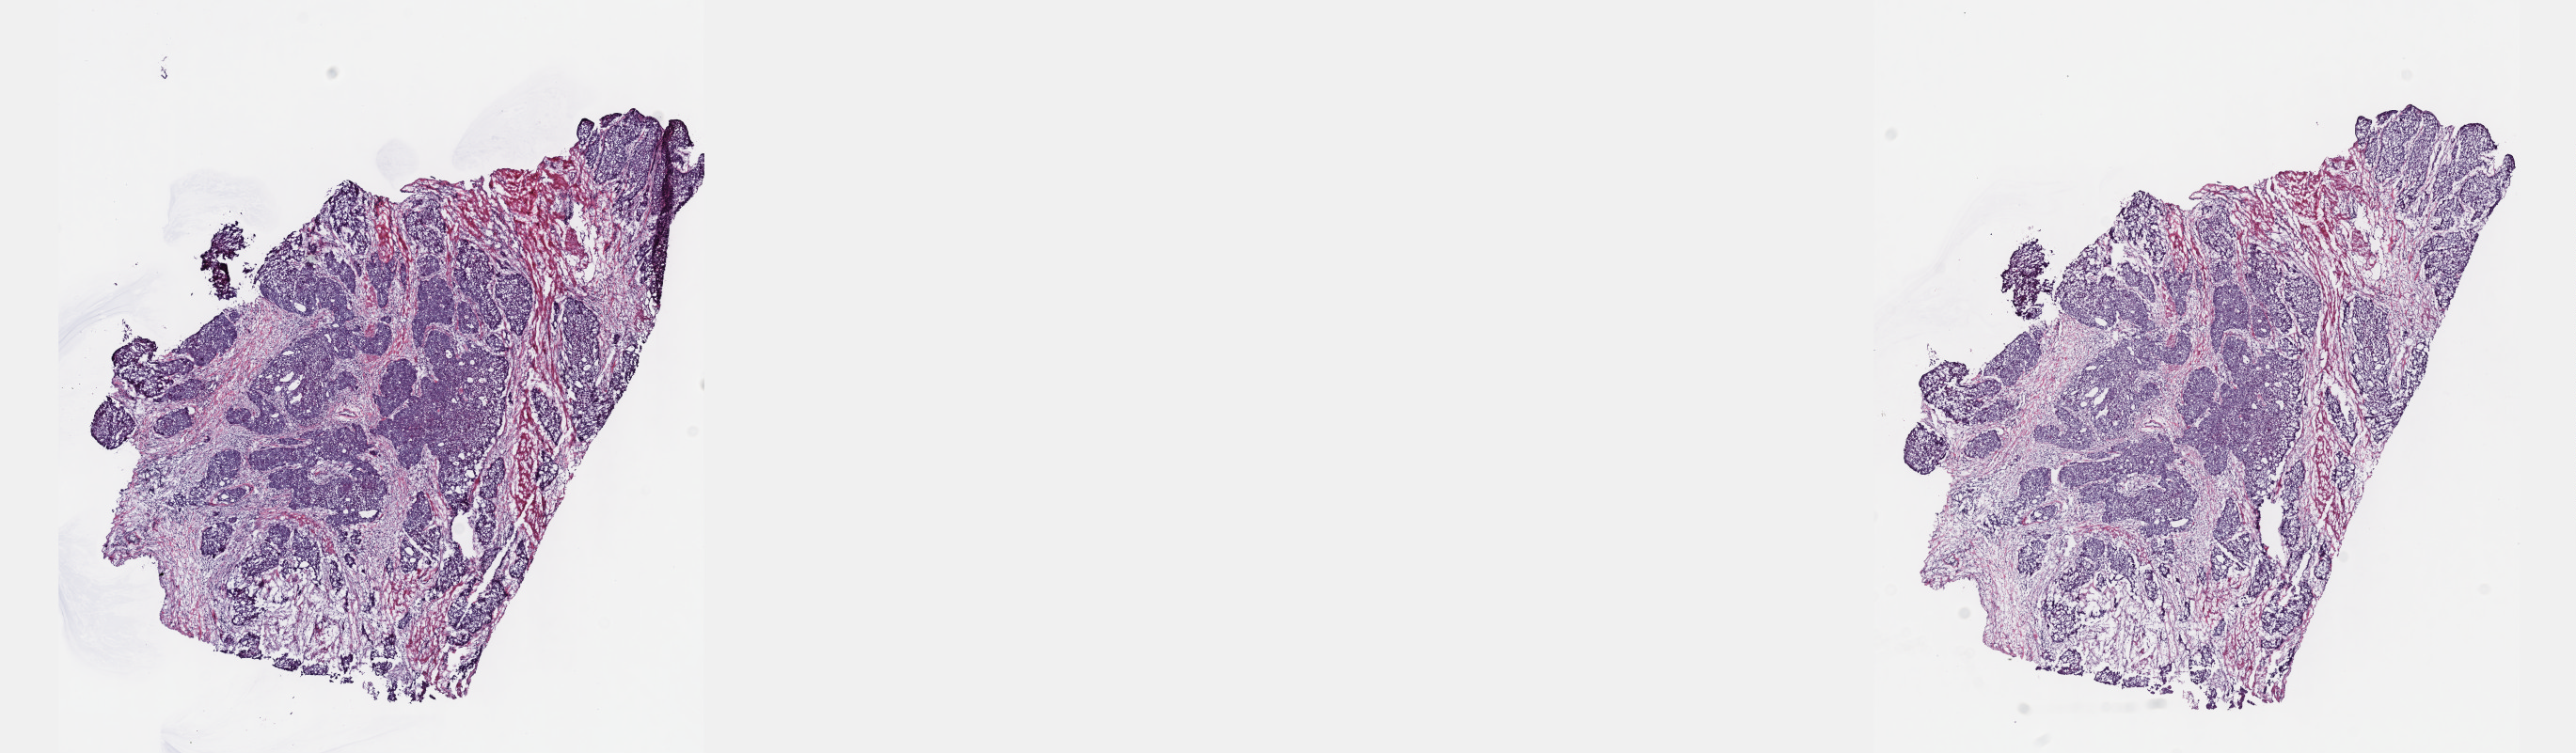
Whole-slide histology image, Hematoxylin and eosin (H&E) stained — whole scanned area (about 22.1 x 6.5 mm) shown as a low-resolution overview; frozen section from the top of the tissue portion; bladder, primary tumour sample. Patient: male, age at initial diagnosis 68 years. Histologic grade: high grade. Pathologist review of this section (percent, as recorded): tumour cells 75%, tumour nuclei 75%, normal cells 0%, stromal cells 25%, necrosis 0%. Inflammatory infiltration, as recorded: lymphocyte infiltration 2%, monocyte infiltration 1%, neutrophil infiltration 5%.
• pathologic diagnosis: Transitional cell carcinoma
• AJCC pathologic stage: III (7th edition)
• lymph nodes positive (case pathology): 0 of 21 examined